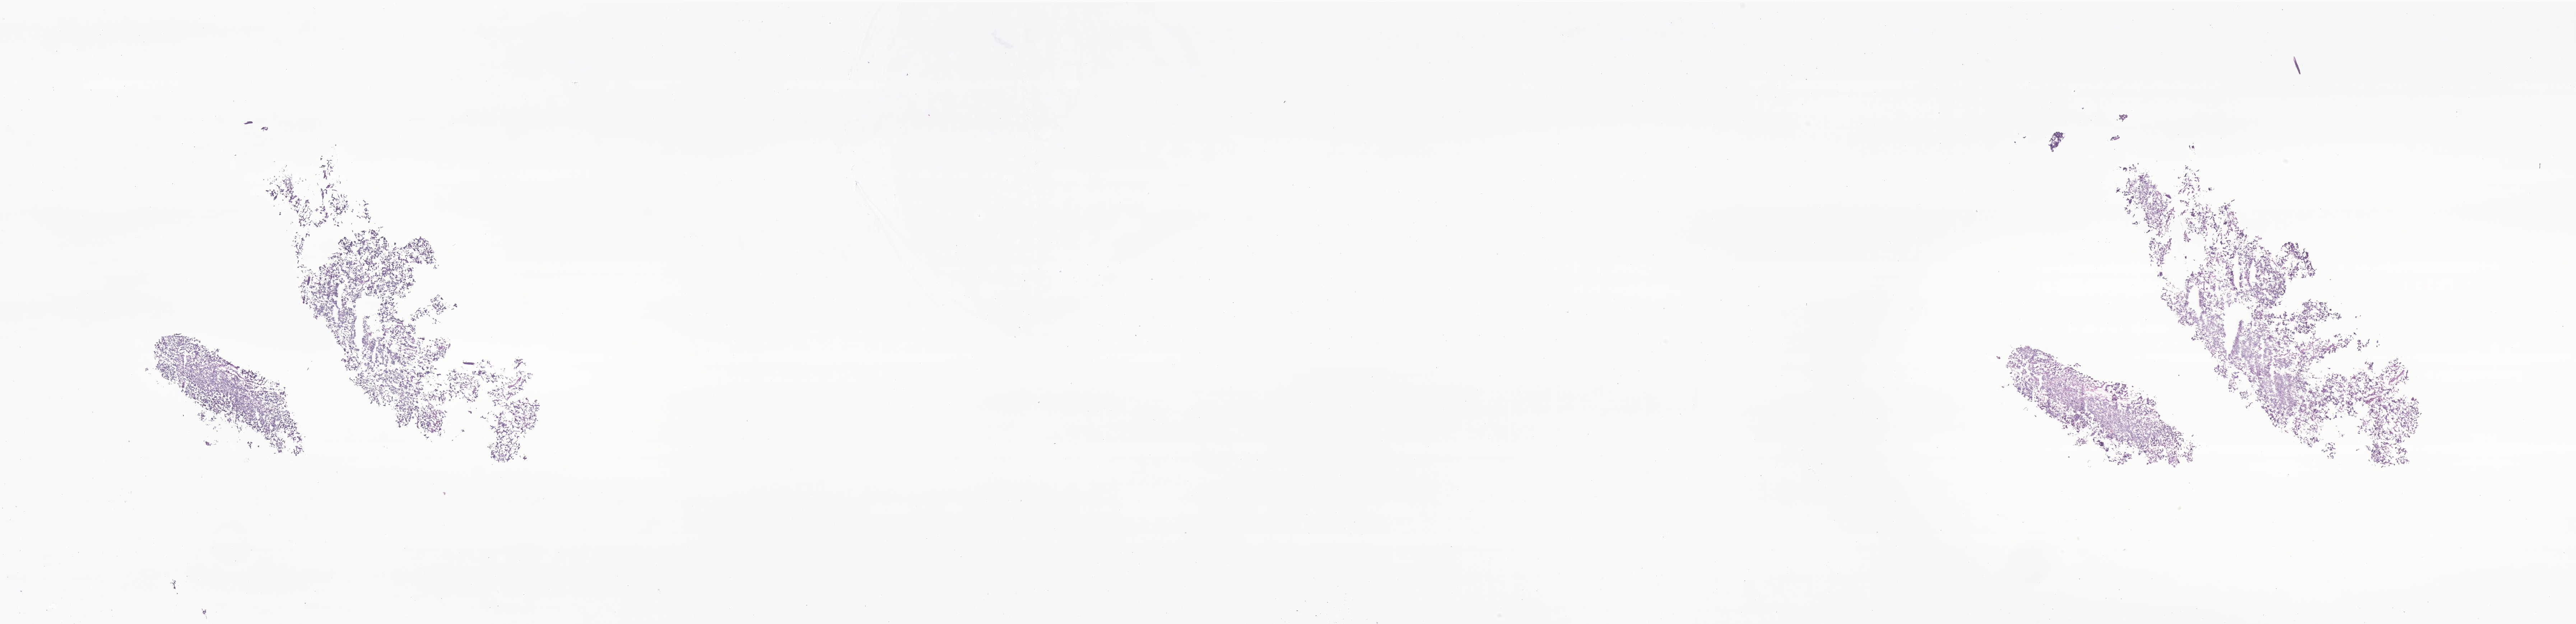
Whole-slide image, H&E stain of tumor tissue from the brain — low-resolution overview of the scanned area, about 30.2 x 7.3 mm. Frozen section. Male patient, age 68 months (5 years 8 months).
Diagnosis (ICD-O-3 morphology term): Tumor cells, malignant.